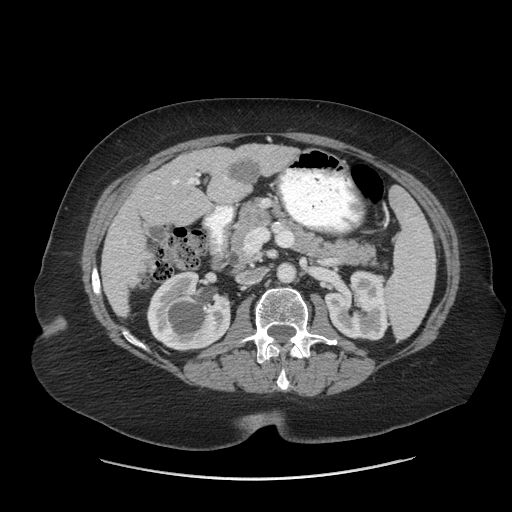
Contrast-enhanced abdominal CT (liver protocol), one axial slice; position 24 of 69 along the scan axis; 140 kVp; soft-tissue window (W 400 / L 40 HU); 2.5 mm slice thickness; 512 × 512 image matrix, field of view 420 × 420 mm. From the clinical record (not read from this slice): diagnosis: hepatocellular carcinoma (patient treated with transarterial chemoembolisation; whether this scan precedes or follows treatment is not stated here); TNM stage (as recorded): Stage-IIIB; Child-Pugh class: A; tumour differentiation: moderately differentiated.
Annotated regions visible in this slice (semi-automatic segmentation, software-assisted and operator-edited):
- liver parenchyma outside the tumour (the mass and vessels are separate outlines, so this box may not span the whole liver): bounding box (x1, y1, x2, y2) in pixels: (102, 144, 298, 316)
- liver vessels: (157, 173, 227, 198)